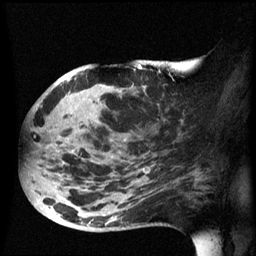
Breast MRI (dynamic contrast-enhanced), one sagittal slice. Slice 28 of 60 in the series (ordered by position). Dynamic contrast-enhanced series, image 2 of 3 at this slice position (ordered by acquisition). 1.5 T. TE 4.2 ms, TR 8.4 ms. 2.5 mm slice thickness. 256 × 256 image matrix. Female patient, age 49 years.
Outlined on this slice (semi-automatically segmented with operator editing):
- analysis volume of interest (the breast-tissue region the enhancement analysis was run in; not a lesion): bounding box <24,72,185,233> (left, top, right, bottom; pixels)
- tumour enhancement mask (voxels above the 70 % enhancement threshold inside the analysis volume of interest): <49,78,71,227>